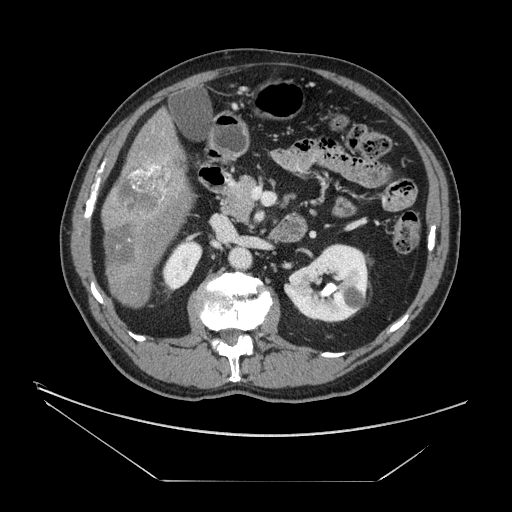
Contrast-enhanced abdominal CT, one axial slice; slice 66 of 161 in the series (ordered by position); reconstruction kernel STANDARD; 120 kVp; intravenous contrast given; soft-tissue window (W 400 / L 40 HU); 2.5 mm slice thickness; 512 × 512 image matrix. Male patient, age 65 years. Case-level facts recorded for this patient, not image findings: diagnosis: colorectal cancer liver metastases, imaged before liver resection; multiple liver metastases: yes; largest metastasis: 4.2 cm; disease in both lobes: yes.
Outlined on this slice (manually delineated by an expert):
- liver: box from (x=103, y=112) to (x=193, y=308) px
- portal vein (with intrahepatic branches): (x=131, y=158)–(x=169, y=192)
- liver metastasis: (x=109, y=227)–(x=136, y=266)
- liver metastasis: (x=118, y=162)–(x=179, y=212)